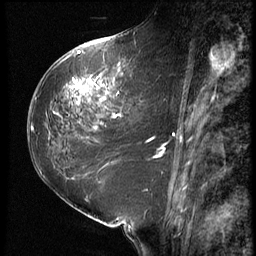
Breast MRI (dynamic contrast-enhanced), one sagittal slice; slice 31 of 64 in the series (ordered by position); 3 images stored at this slice position (order not interpretable as contrast timing); 1.5 T; TE 4.2 ms, TR 9 ms; 256 × 256 image matrix. Patient: female, 59 years. Case-level facts recorded for this patient, not image findings: setting: breast cancer imaged before/during neoadjuvant chemotherapy; receptor status: HER2-positive.
Annotated regions visible in this slice (semi-automatically segmented with operator editing):
- analysis volume of interest (the breast-tissue region the enhancement analysis was run in; not a lesion): bounding box (x1, y1, x2, y2) in pixels: (54, 65, 155, 132)
- tumour enhancement mask (voxels above the 140 % enhancement threshold inside the analysis volume of interest): (54, 65, 122, 117)